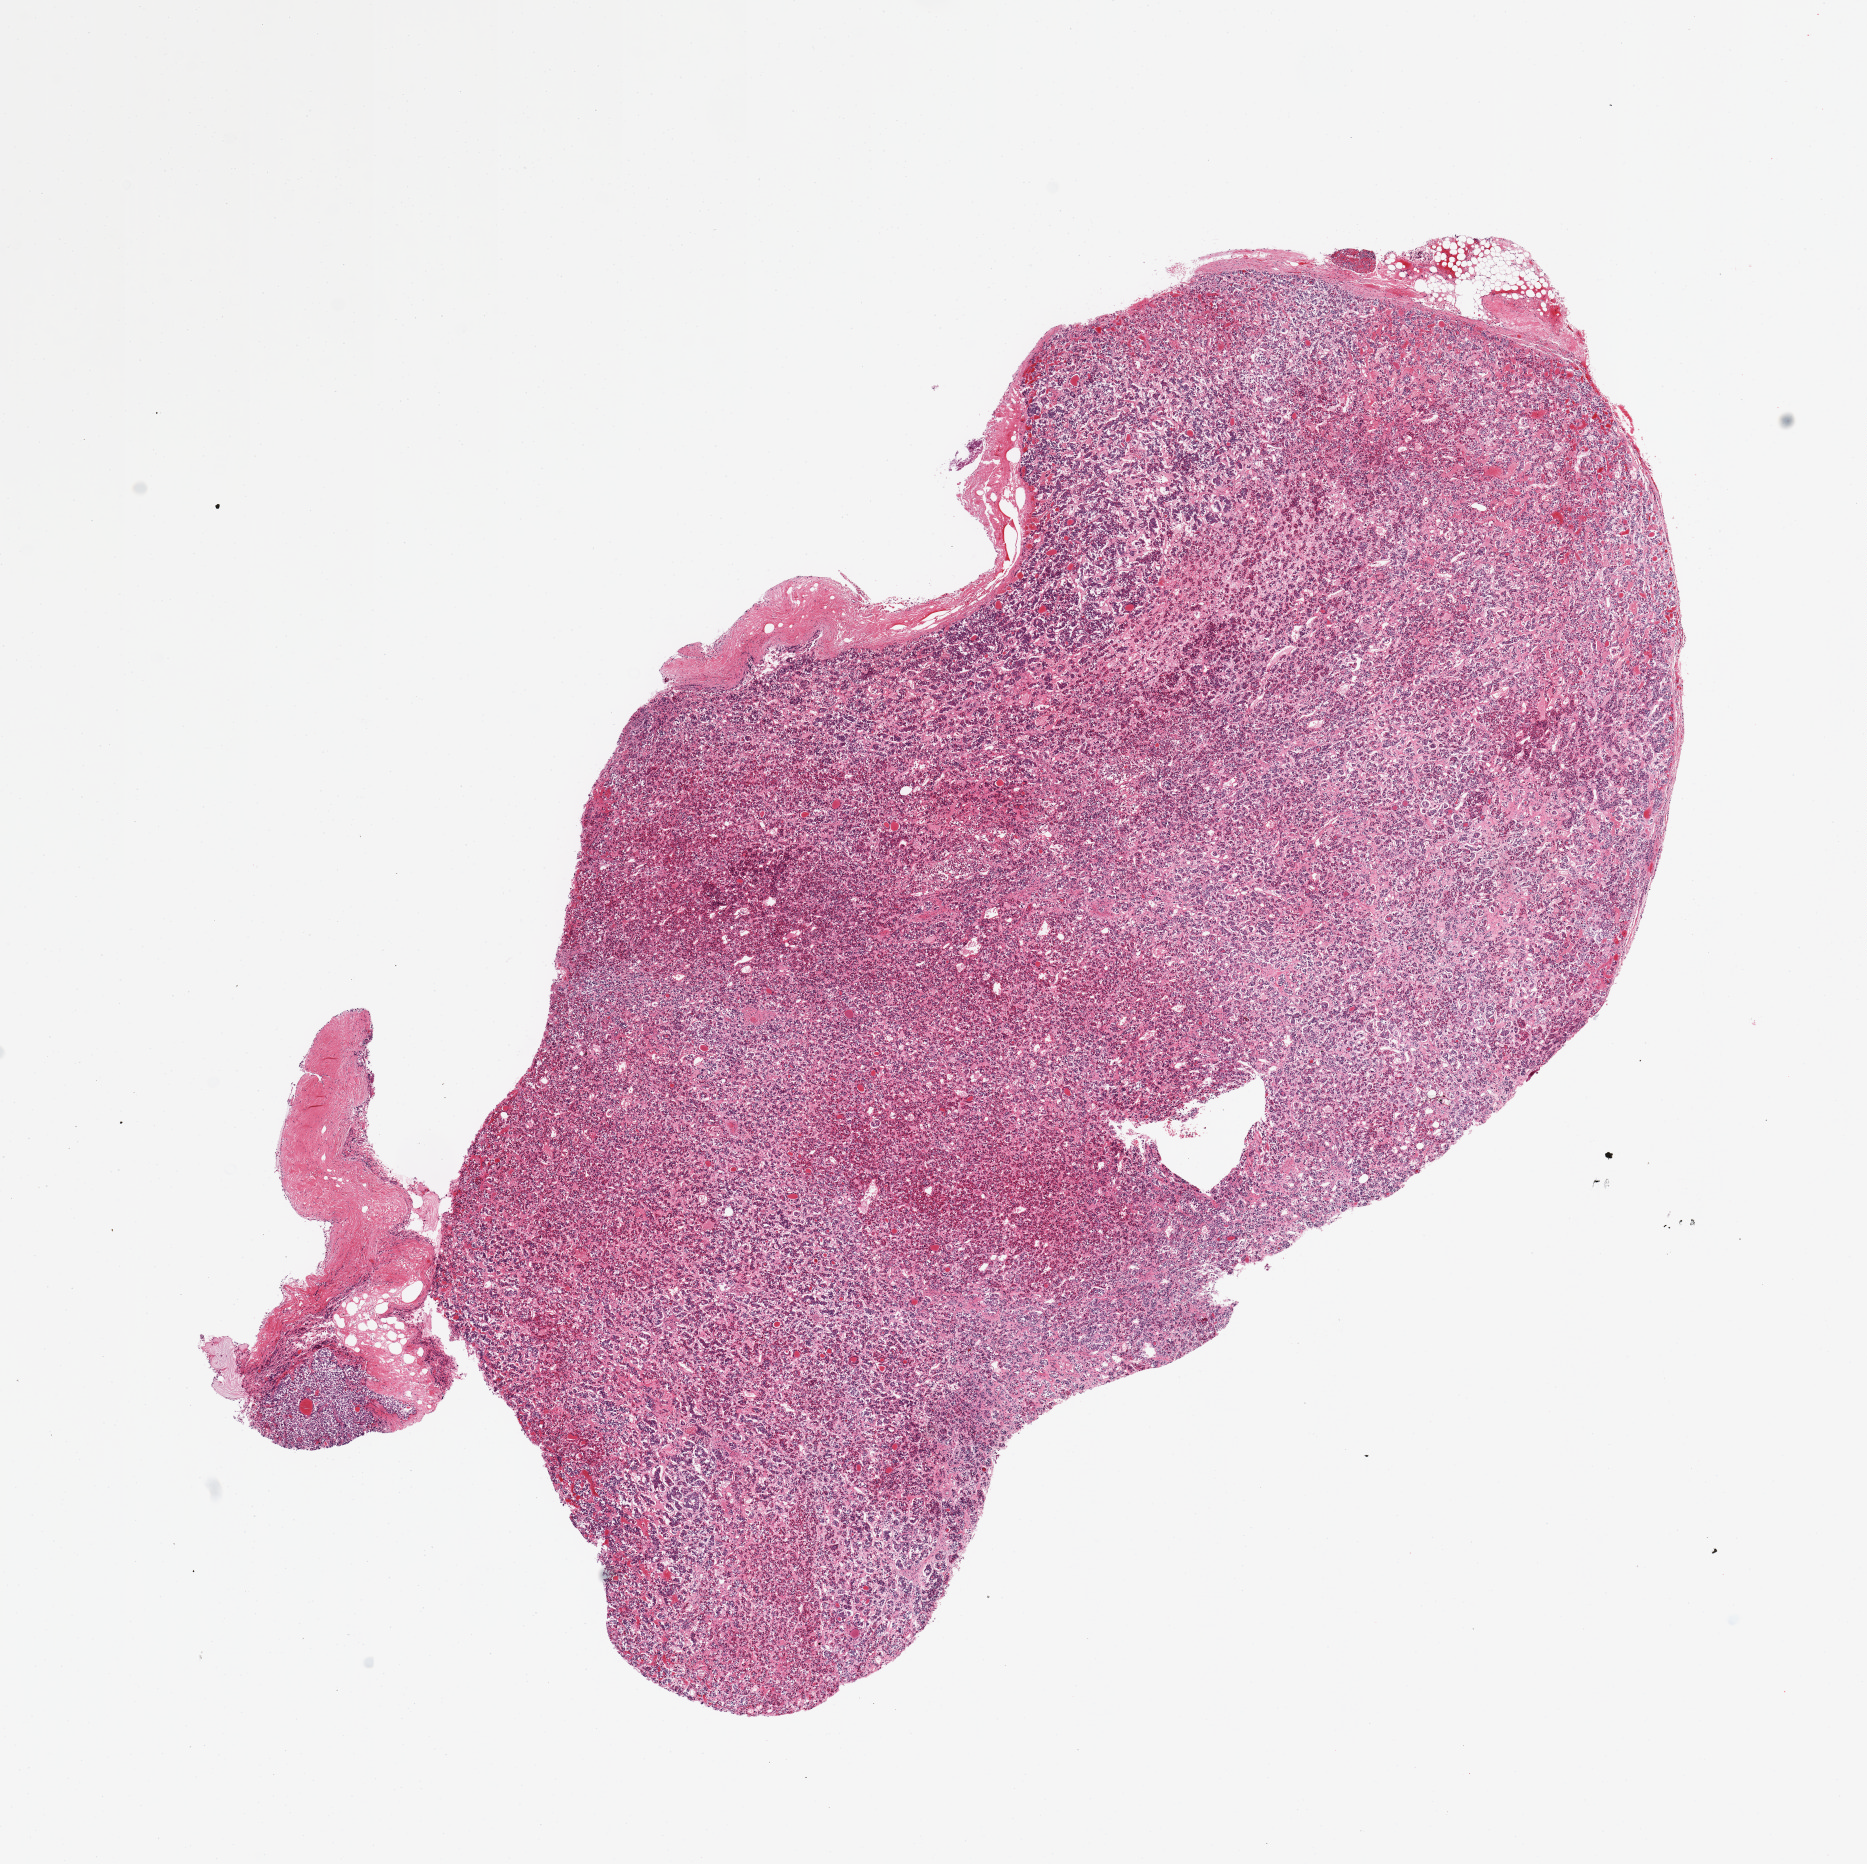
Whole-slide image, hematoxylin and eosin (H&E) stain, brightfield, shown as a low-resolution overview of the whole scanned area (about 14.8 x 14.7 mm, slide scanned at 20x); PAXgene-fixed, paraffin-embedded tissue; target tissue: pituitary; donor tissue sample. Female donor.
* pathologist's review note for this sample: 1 piece, adenohypophysis; trace dura